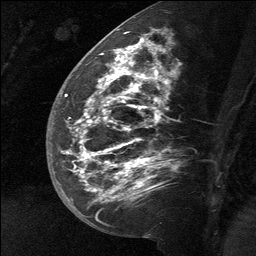
Breast MRI (dynamic contrast-enhanced), one sagittal slice; slice 29 of 64 in the series (ordered by position); dynamic contrast-enhanced study with each time point stored as its own series, time point 2 of 3 at this slice position (early post-contrast, ordered by acquisition time); 1.5 T; TE 4.8 ms, TR 27 ms; 256 × 256 image matrix, field of view 180 × 180 mm. Female patient, age 39 years. From the clinical record (not read from this slice): setting: breast cancer imaged before/during neoadjuvant chemotherapy; receptor status: HER2-positive.
Annotated regions visible in this slice (semi-automatic segmentation, software-assisted and operator-edited):
- analysis volume of interest (the breast-tissue region the enhancement analysis was run in; not a lesion): bounding box [x1, y1, x2, y2] px = [58, 40, 170, 217]
- tumour enhancement mask (voxels above the 90 % enhancement threshold inside the analysis volume of interest): [65, 40, 153, 198]